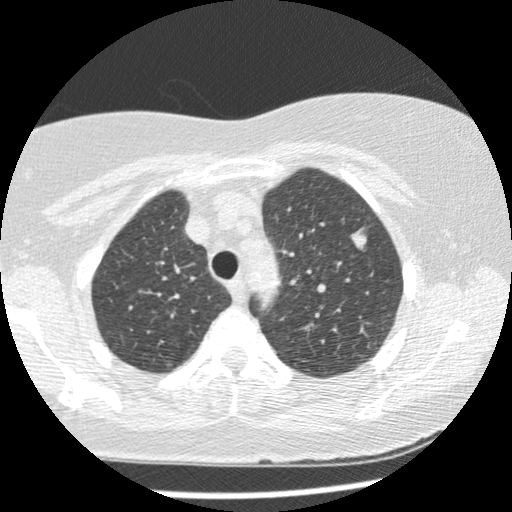
Low-dose screening chest CT, one axial slice. Slice 183 of 241 in the series (ordered by position). 120 kVp. Lung window (W 1500 / L -600 HU). 512 × 512 image matrix.
Structures marked on this image (expert manual segmentation):
- lesion 2 (tumor, upper lobe of left lung): bounding box [x1, y1, x2, y2] px = [350, 227, 367, 251]